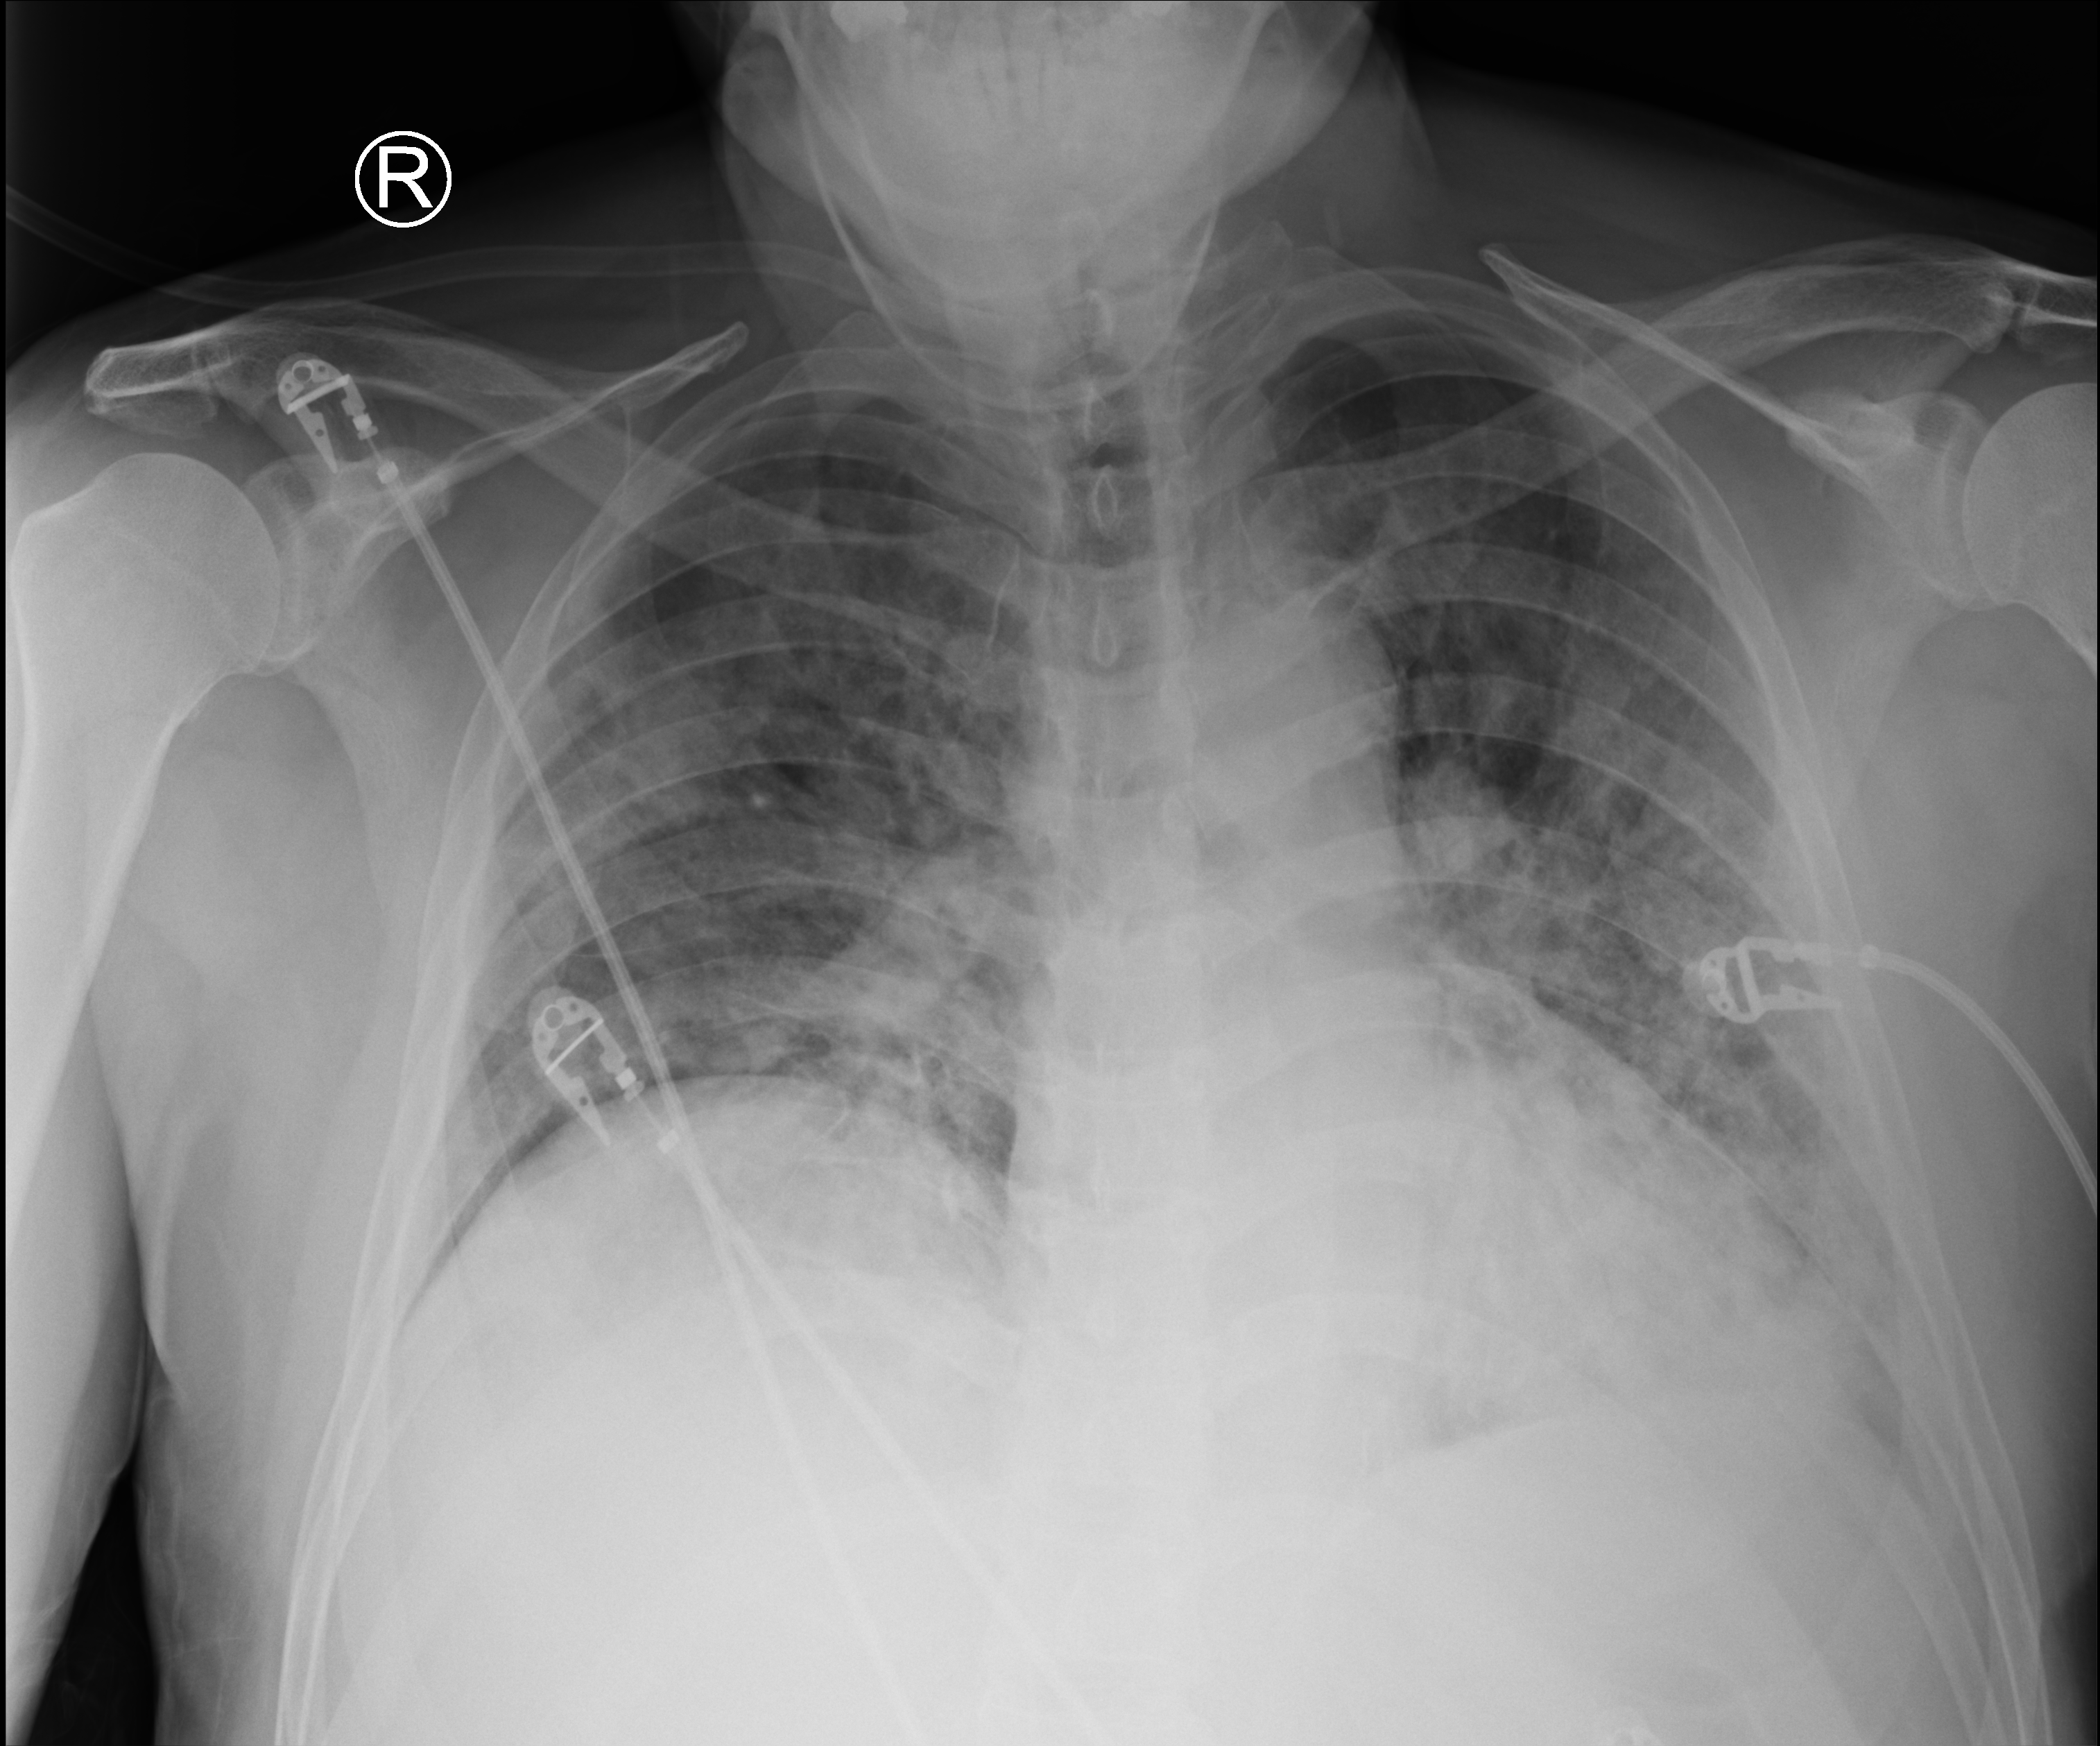
Bedside chest radiograph (computed radiography). Male patient hospitalised with COVID-19, age 60–74 years.
From the hospital-stay record, not from the radiograph (when in the stay this image was taken is not recorded): chronic kidney disease (admission record): no; mechanically ventilated during this hospital stay: no.